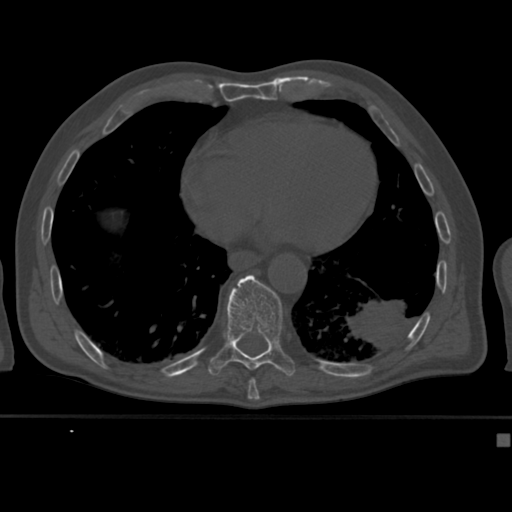
CT including the spine, one axial slice; slice 231 of 430 in the series (ordered by position); bone window (W 1800 / L 400 HU); 1.5 mm slice thickness; 512 × 512 image matrix, field of view 337 × 337 mm. Patient: male, 64 years. From the clinical record (not read from this slice): primary cancer: uterus; vertebrae with lytic lesions (as recorded): T1, T4, T5, T7, L5.
Structures marked on this image (semi-automatic segmentation, software-assisted and operator-edited):
- T10 vertebra: bounding box [x1, y1, x2, y2] px = [208, 274, 295, 377]
- T9 vertebra: [250, 378, 256, 382]